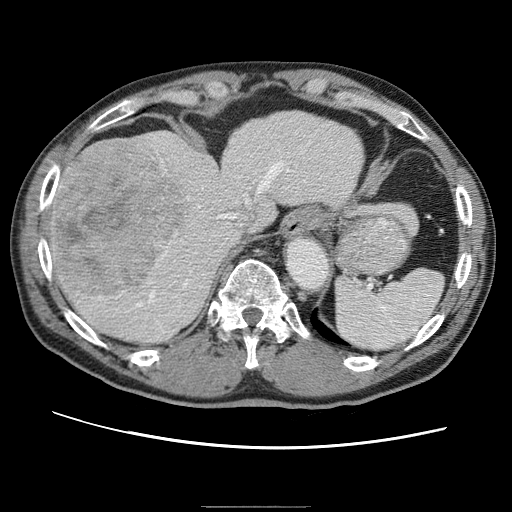
Contrast-enhanced abdominal CT (liver protocol), one axial slice. Position 49 of 75 along the scan axis. One of 2 acquisitions stored at this slice position. Soft-tissue window (W 400 / L 40 HU). 512 × 512 image matrix, field of view 360 × 360 mm. Case-level facts recorded for this patient, not image findings: diagnosis: hepatocellular carcinoma (patient treated with transarterial chemoembolisation; whether this scan precedes or follows treatment is not stated here); TNM stage (as recorded): Stage-II; Child-Pugh class: A; tumour differentiation: well differentiated; tumour nodularity: multinodular.
Annotated regions visible in this slice (semi-automatic segmentation, software-assisted and operator-edited):
- abdominal aorta: bounding box [x1, y1, x2, y2] px = [284, 237, 327, 289]
- liver parenchyma outside the tumour (the mass and vessels are separate outlines, so this box may not span the whole liver): [48, 112, 368, 342]
- mass: [51, 143, 188, 301]
- liver vessels: [126, 146, 289, 313]